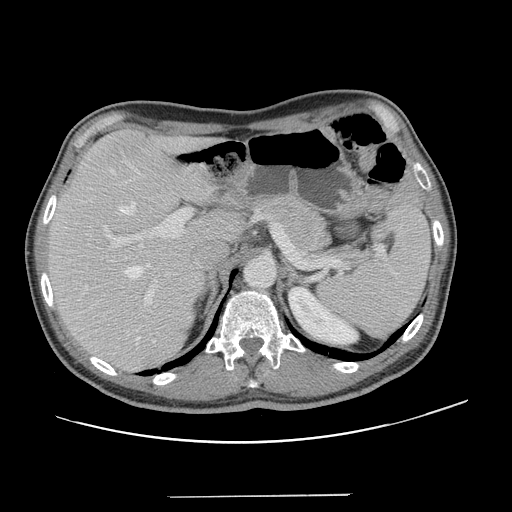
Contrast-enhanced abdominal CT, one axial slice; position 90 of 131 along the scan axis; 120 kVp; soft-tissue window (W 400 / L 40 HU); 2.5 mm slice thickness; 512 × 512 image matrix, field of view 403 × 403 mm. Male patient, age 60 years. Case-level facts recorded for this patient, not image findings: diagnosis: colorectal cancer liver metastases, imaged before liver resection; multiple liver metastases: no; largest metastasis: 2.5 cm; disease in both lobes: no.
Outlined on this slice (expert manual segmentation):
- hepatic veins: box from (x=110, y=170) to (x=150, y=279) px
- liver: (x=47, y=129)–(x=241, y=371)
- planned liver remnant (the part of the liver to remain after resection): (x=47, y=129)–(x=241, y=355)
- portal vein (with intrahepatic branches): (x=103, y=161)–(x=192, y=303)